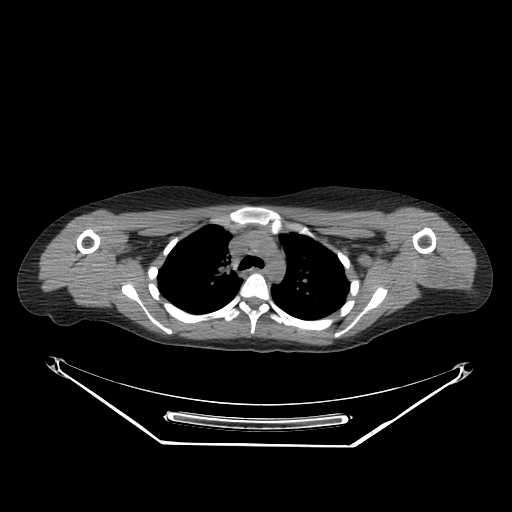
CT of an extremity soft-tissue mass (from a PET/CT study), one axial slice. Slice 204 of 267 in the series (ordered by position). Reconstruction kernel SOFT. 140 kVp. Soft-tissue window (W 400 / L 40 HU). 3.75 mm slice thickness. 512 × 512 image matrix, field of view 500 × 500 mm. Female patient. Case-level facts recorded for this patient, not image findings: histological type: malignant fibrous histiocytoma; grade: low; site of the primary tumour: left arm.
Annotated regions visible in this slice (expert contour drawn on MRI and transferred to this co-registered scan by the dataset authors):
- gross tumour volume (mass): bounding box <422,251,458,282> (left, top, right, bottom; pixels)